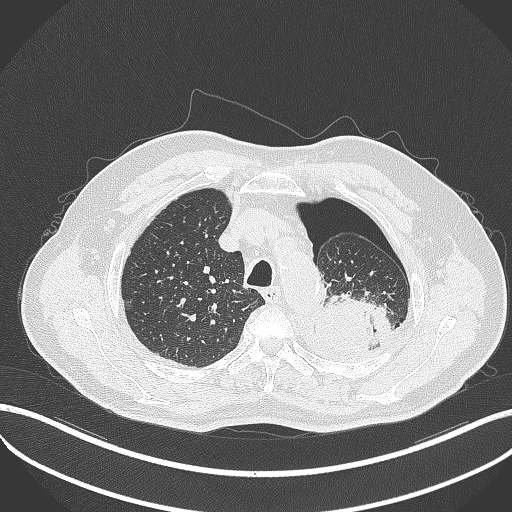
Chest CT, one axial slice. Position 400 of 464 along the scan axis. Reconstruction kernel B70f. Lung window (W 1500 / L -600 HU). 512 × 512 image matrix, field of view 400 × 400 mm. Male patient, age 76 years. Case-level facts recorded for this patient, not image findings: clinical TNM (as recorded): T3 N0 M1b.
Outlined on this slice (rectangle marked by the reading radiologist):
- lung tumour (recorded histology: adenocarcinoma): bounding box [x1, y1, x2, y2] px = [315, 289, 394, 356]